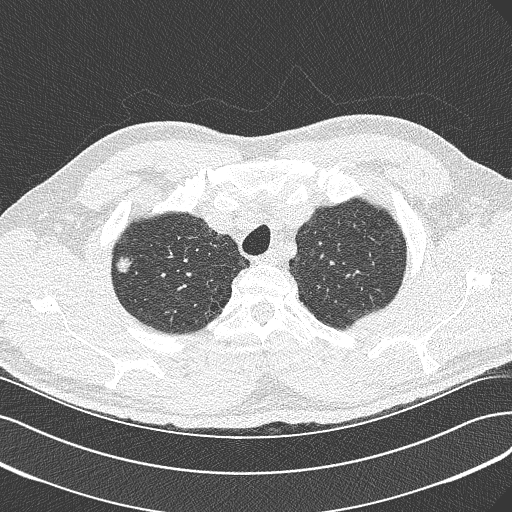
Chest CT (low-dose screening protocol), one axial image; first (baseline) screen; lung window (W 1500 / L -600 HU); 120 kVp; 512 × 512 image matrix. Male, age 56 years at enrolment. Current smoker at enrolment.
Lesion marked by an expert reader, bounding box (x1, y1, x2, y2) in pixels: (104, 248, 143, 285). The exam's reader record, not a measurement of the box and not confirmed to be the same lesion: non-calcified nodule or mass ≥4 mm, right upper lobe, 10 × 7 mm, spiculated (stellate) margins, soft tissue attenuation.